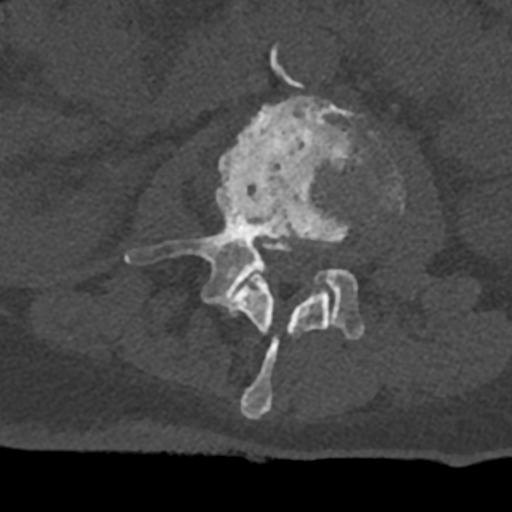
CT including the spine, one axial slice; position 345 of 797 along the scan axis; 120 kVp; bone window (W 1800 / L 400 HU); 512 × 512 image matrix. Patient: male, 74 years. Case-level facts recorded for this patient, not image findings: primary cancer: renal; vertebrae with lytic lesions (as recorded): T10, L1, L2, L3, L4, L5.
Annotated regions visible in this slice (semi-automatically segmented with operator editing):
- L2 vertebra: bounding box <228,265,331,419> (left, top, right, bottom; pixels)
- L3 vertebra: <125,95,404,340>